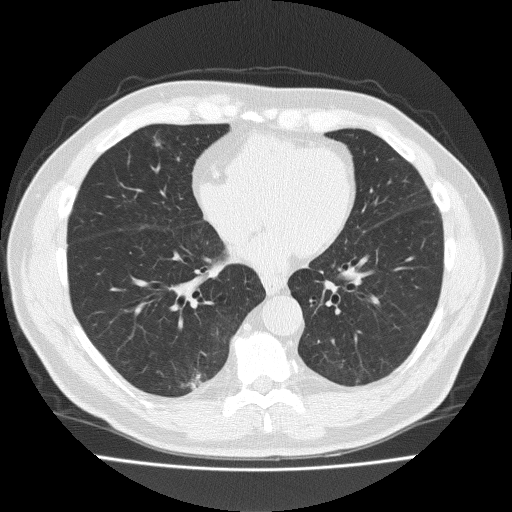
Axial slice from a low-dose chest CT screening exam, second annual screen, lung window (W 1500 / L -600 HU), 2 mm slice thickness, slice 114 of 184 in the series. Male participant, aged 57 years at enrolment. Current smoker at enrolment.
Expert reader's lesion annotation, bounding box <136,129,178,170> (left, top, right, bottom; pixels). The exam's reader record, not a measurement of the box and not confirmed to be the same lesion: non-calcified nodule or mass ≥4 mm, right middle lobe, 8 × 7 mm, spiculated (stellate) margins, soft tissue attenuation, pre-existing on the prior screen: yes; interval growth: yes.